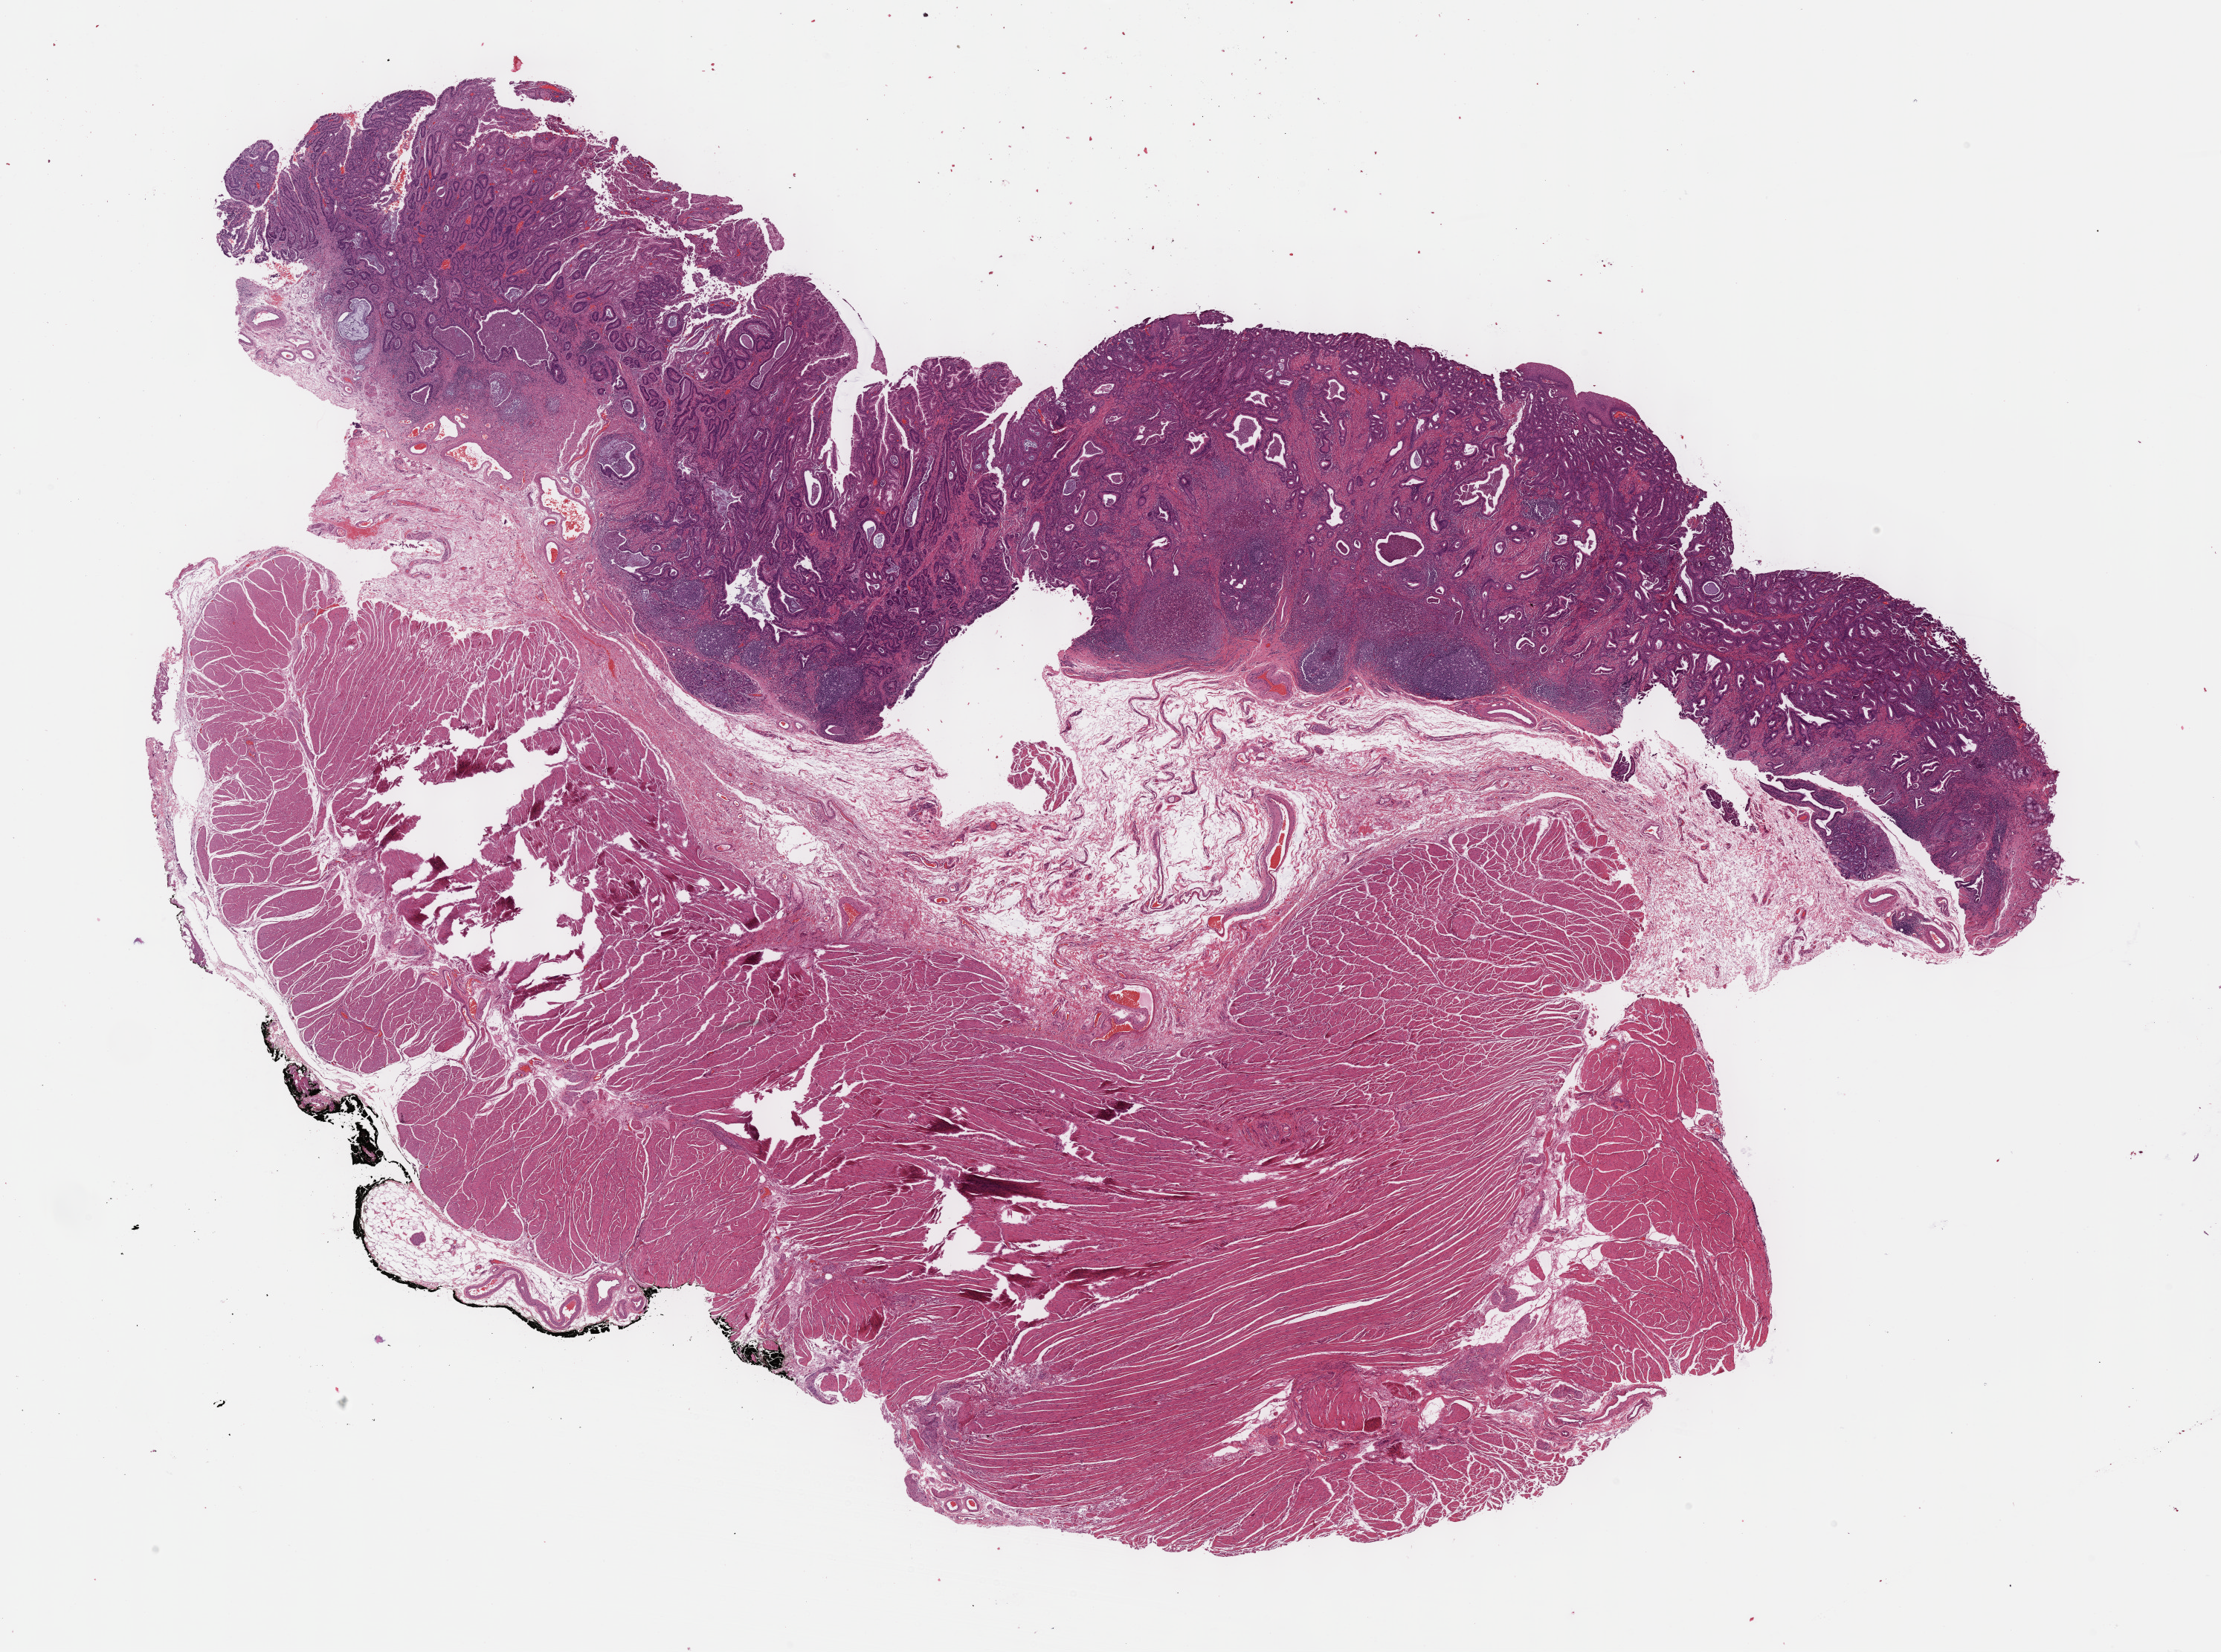
Digitized Hematoxylin and eosin (H&E) stained tissue section (whole slide) — whole scanned area (about 24.2 x 18.0 mm) shown as a low-resolution overview, formalin-fixed paraffin-embedded (FFPE) diagnostic section, esophagus, primary tumour sample. Male, age 69 years at initial diagnosis. Histologic grade: G1 (well differentiated).
* lymph nodes positive (case pathology): 0 of 26 examined
* diagnosis: Adenocarcinoma, NOS (lower third of esophagus)